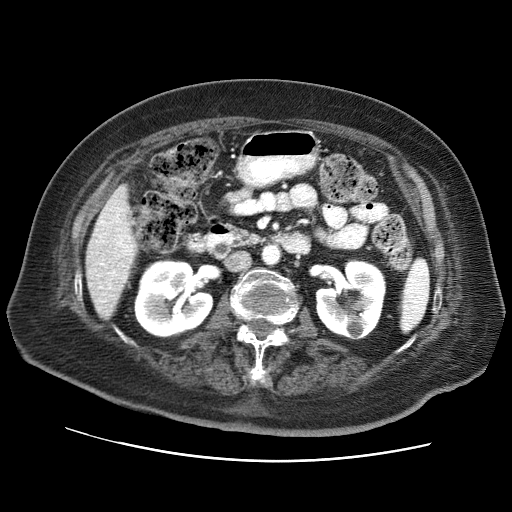
Contrast-enhanced abdominal CT (liver protocol), one axial slice; position 23 of 73 along the scan axis; reconstruction kernel STANDARD; 120 kVp; soft-tissue window (W 400 / L 40 HU); 2.5 mm slice thickness; 512 × 512 image matrix, field of view 380 × 380 mm. From the clinical record (not read from this slice): diagnosis: hepatocellular carcinoma (patient treated with transarterial chemoembolisation; whether this scan precedes or follows treatment is not stated here); TNM stage (as recorded): Stage-I; Child-Pugh class: A; tumour differentiation: well differentiated; tumour nodularity: uninodular.
Annotated regions visible in this slice (semi-automatic segmentation, software-assisted and operator-edited):
- liver parenchyma outside the tumour (the mass and vessels are separate outlines, so this box may not span the whole liver): bounding box <86,185,136,318> (left, top, right, bottom; pixels)
- liver vessels: <97,207,132,302>